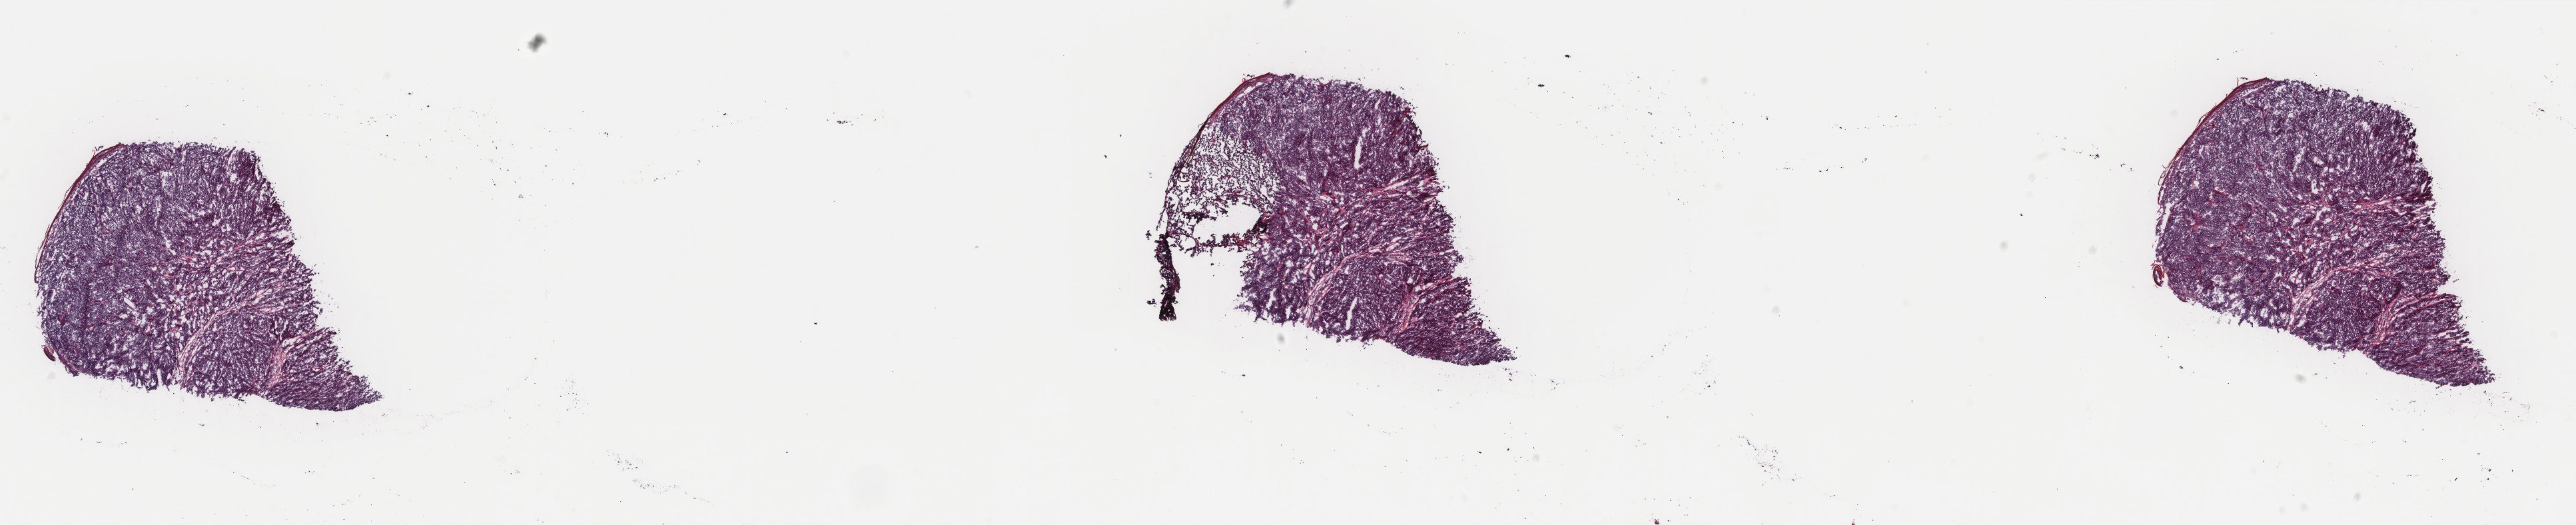
Whole-slide histology image, Hematoxylin and eosin (H&E) stained, whole scanned area (about 30.7 x 6.3 mm, acquisition: 40x scan) shown as a low-resolution overview; frozen section; primary tumour sample from the skin. Patient sex: male. Slide review estimates, as recorded: tumour cells 100%, tumour nuclei 97%, normal cells 0%, stromal cells 0%, necrosis 0%. Infiltration values recorded for this section: lymphocyte infiltration 0%, monocyte infiltration 0%, neutrophil infiltration 0%.
AJCC pathologic stage: IIC (7th edition). Pathologic diagnosis: Spindle cell melanoma, NOS.